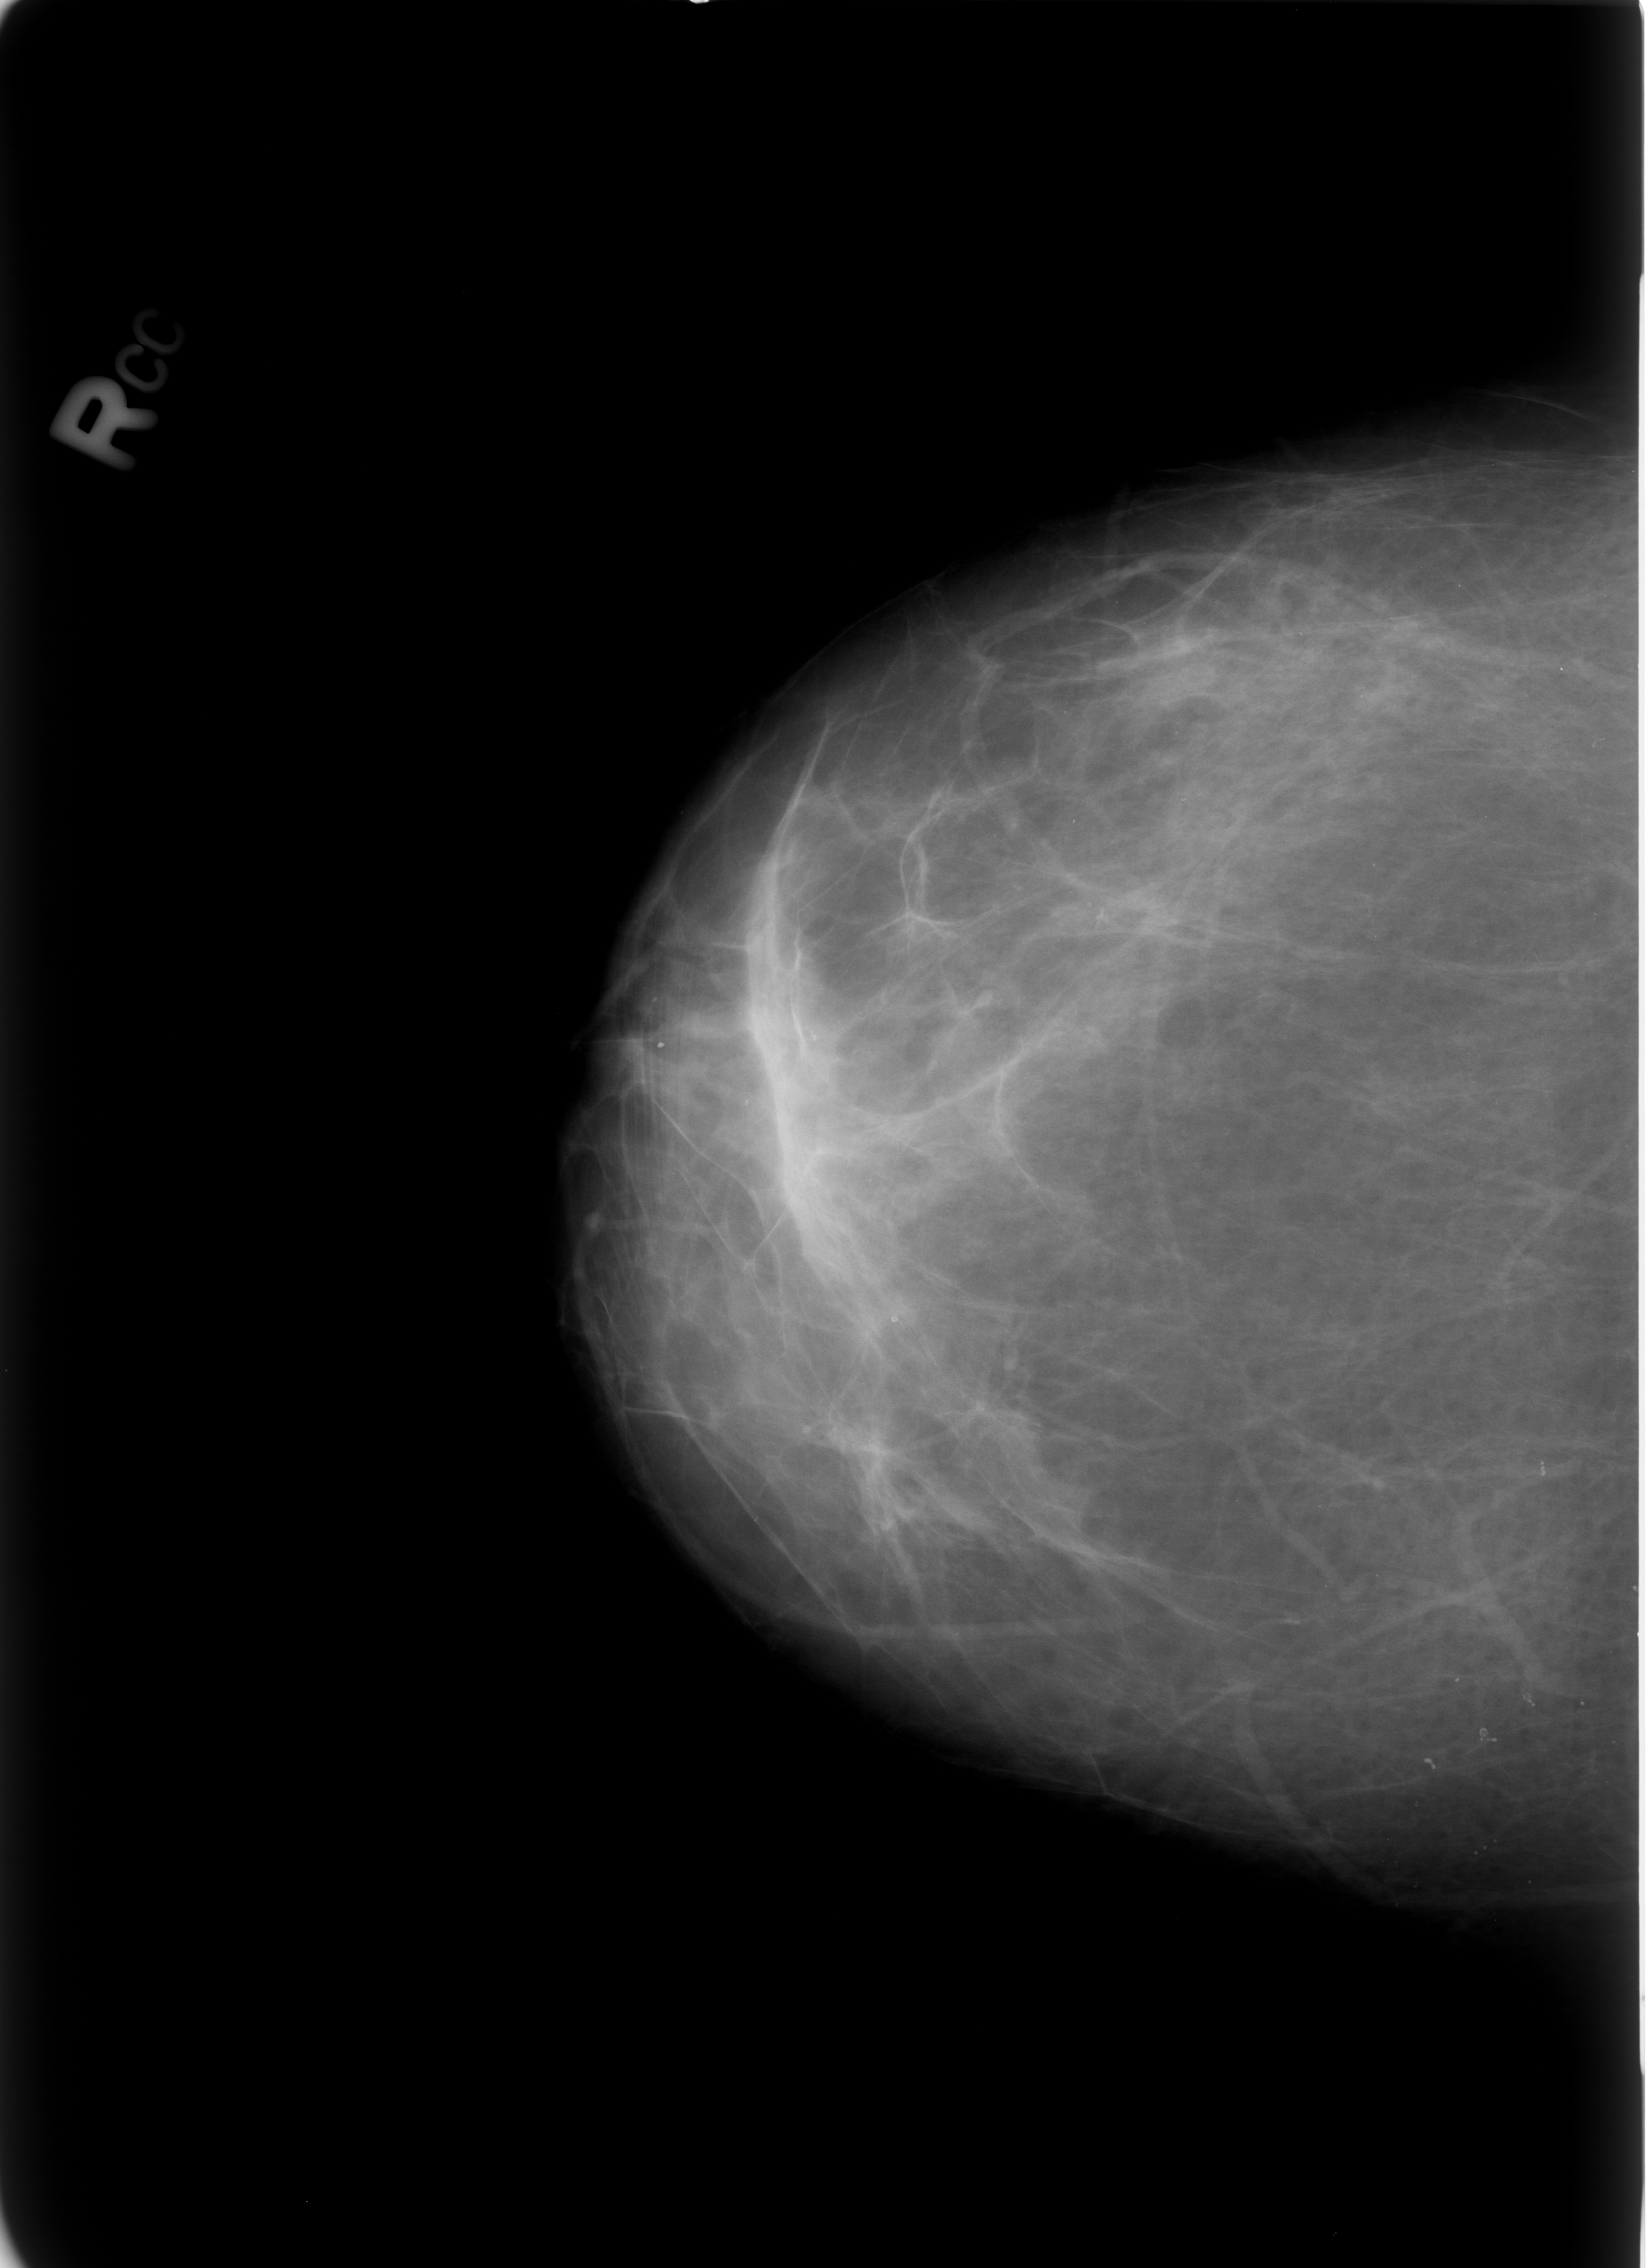
Mammogram (digitized film); right breast; craniocaudal (CC) view; BI-RADS breast density category 2 (scale 1–4).
Marked abnormality: calcifications, morphology skin, distribution regional; BI-RADS assessment category 2; benign without callback (not worked up further).